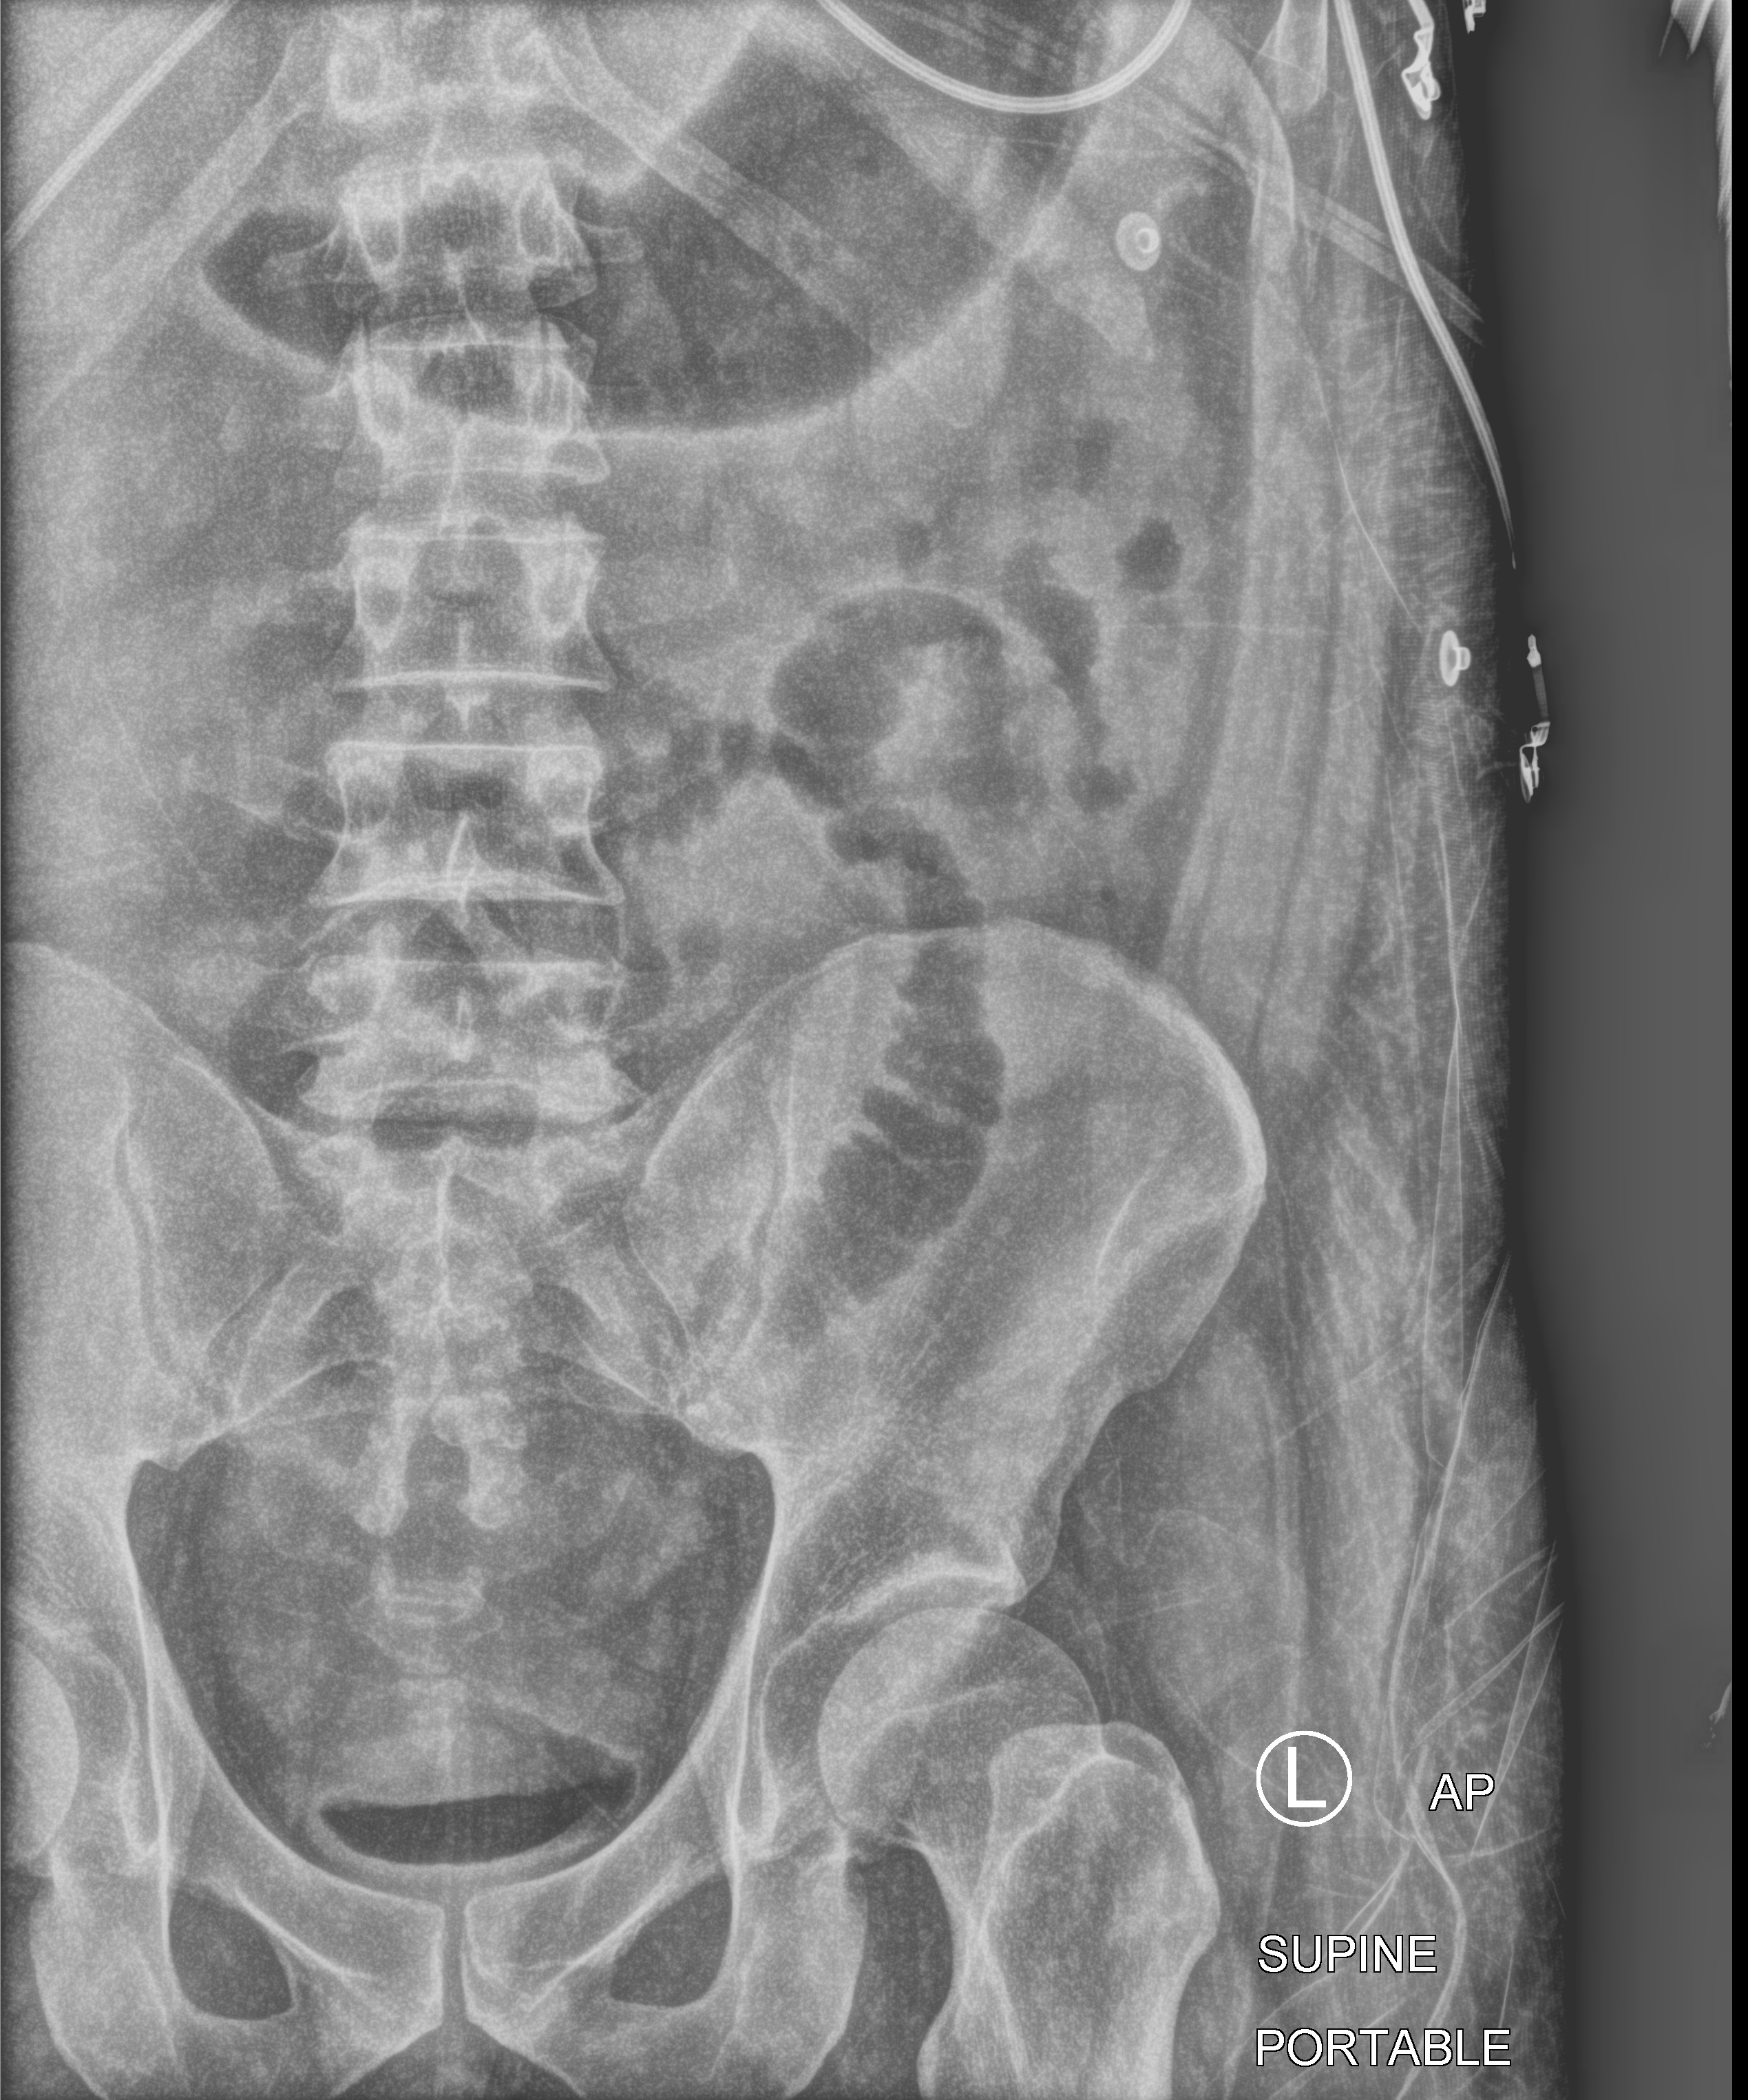
Bedside abdomen radiograph (computed radiography), anteroposterior (AP) projection. Patient hospitalised with COVID-19; male, aged 18–59 years.
Admission-level facts for this patient (not findings on this image; timing relative to this image not recorded):
- admitted to intensive care during this hospital stay: yes
- smoking status (admission record): current